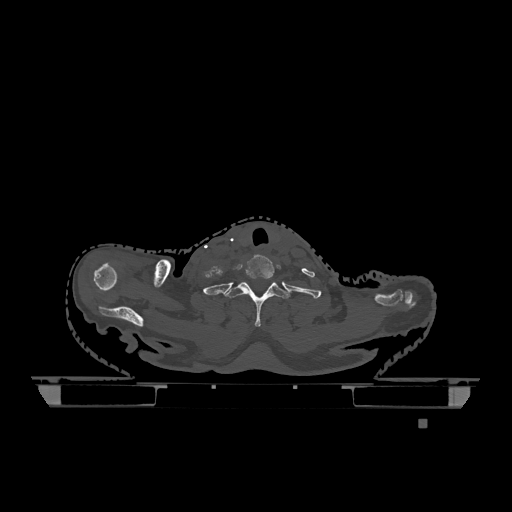
CT including the spine, one axial slice; slice 1008 of 1317 in the series (ordered by position); bone window (W 1800 / L 400 HU); 0.5 mm slice thickness; 512 × 512 image matrix, field of view 500 × 500 mm. Female patient, age 74 years. Case-level facts recorded for this patient, not image findings: primary cancer: lung.
Structures marked on this image (semi-automatic segmentation, software-assisted and operator-edited):
- T1 vertebra: bounding box <223,282,290,327> (left, top, right, bottom; pixels)